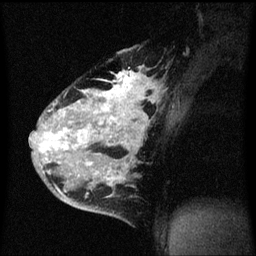
Breast MRI (dynamic contrast-enhanced), one sagittal slice. Slice 43 of 60 in the series (ordered by position). Dynamic contrast-enhanced series, image 2 of 3 at this slice position (ordered by acquisition). 1.5 T. TE 4.2 ms, TR 8.4 ms. 256 × 256 image matrix, field of view 200 × 200 mm. Patient: female, 34 years. Case-level facts recorded for this patient, not image findings: setting: breast cancer imaged before/during neoadjuvant chemotherapy; receptor status: HR-positive, HER2-negative.
Annotated regions visible in this slice (semi-automatic segmentation, software-assisted and operator-edited):
- analysis volume of interest (the breast-tissue region the enhancement analysis was run in; not a lesion): bounding box <34,50,159,215> (left, top, right, bottom; pixels)
- tumour enhancement mask (voxels above the 70 % enhancement threshold inside the analysis volume of interest): <34,72,153,187>